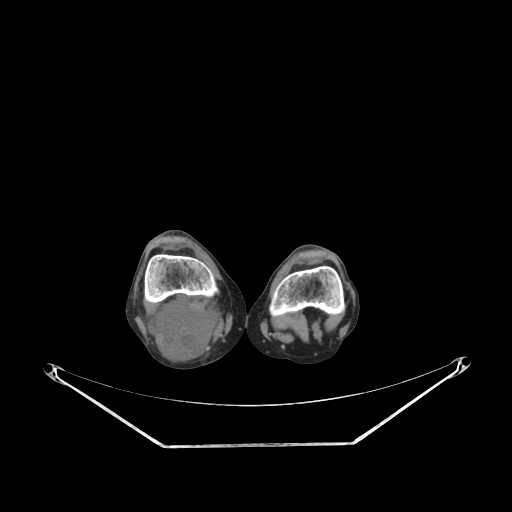
CT of an extremity soft-tissue mass (from a PET/CT study), one axial slice; position 172 of 267 along the scan axis; reconstruction kernel SOFT; 140 kVp; soft-tissue window (W 400 / L 40 HU); 3.75 mm slice thickness; 512 × 512 image matrix, field of view 500 × 500 mm. Female patient. Case-level facts recorded for this patient, not image findings: histological type: liposarcoma; site of the primary tumour: right thigh.
Annotated regions visible in this slice (expert contour drawn on MRI and transferred to this co-registered scan by the dataset authors):
- gross tumour volume (mass): box from (x=148, y=295) to (x=222, y=360) px